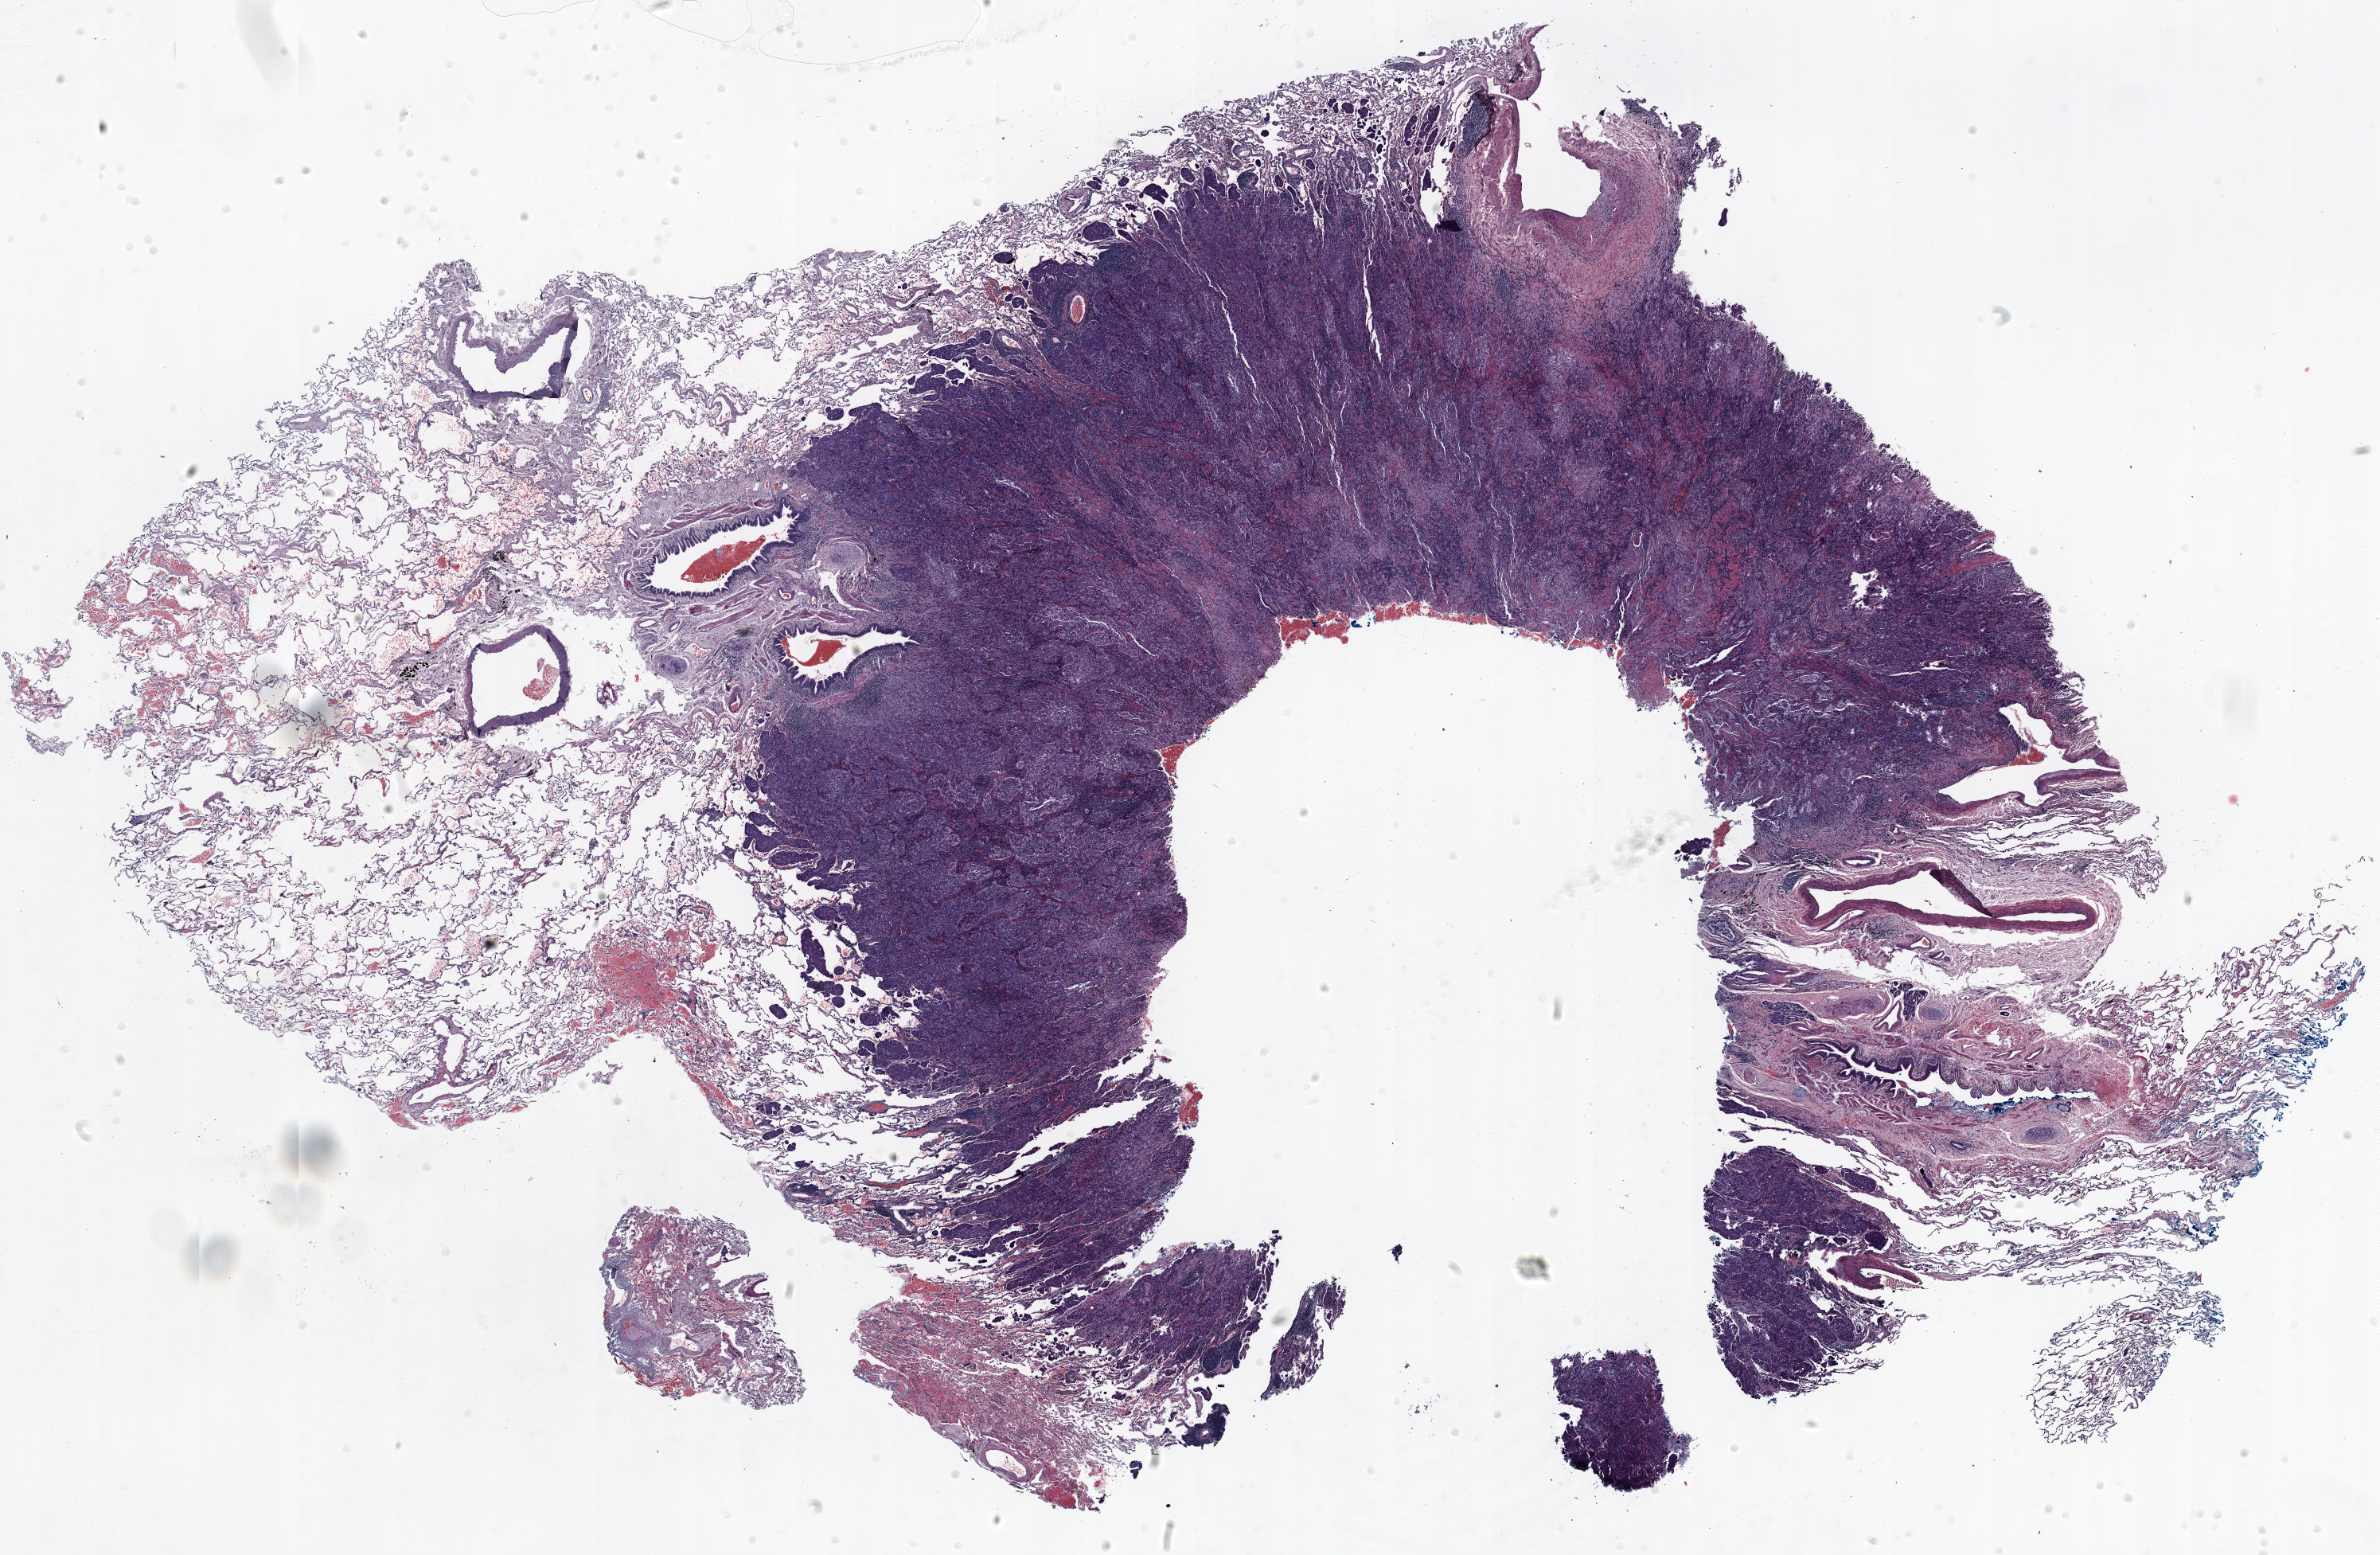
H&E-stained whole-slide image, shown as a low-resolution overview of the whole scanned area (about 24.0 x 15.7 mm, from a 20x scan); formalin-fixed paraffin-embedded (FFPE) section; lung tissue. Male, age 65 at enrolment. Grade: poorly differentiated (G3).
Primary tumour location (clinical record): right lower lobe. Stage (AJCC 6th edition): IA. Participant's lung-cancer diagnosis: Adenocarcinoma, NOS (ICD-O-3 8140/3). Tumour size (pathology): 18 mm.